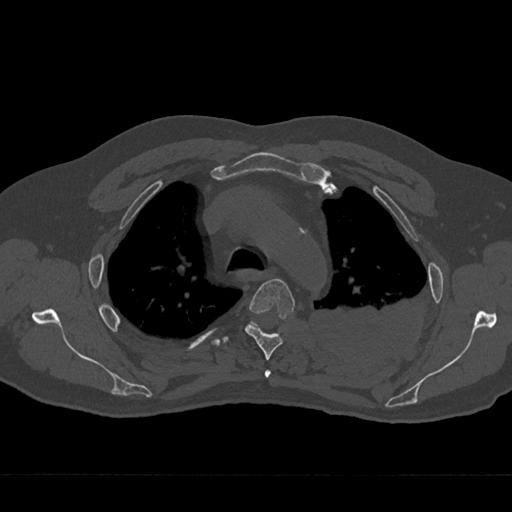
CT including the spine, one axial slice. Slice 517 of 797 in the series (ordered by position). Reconstruction kernel Br40s/3. Bone window (W 1800 / L 400 HU). 512 × 512 image matrix, field of view 377 × 377 mm. Patient: male, 75 years. From the clinical record (not read from this slice): primary cancer: renal.
Structures marked on this image (semi-automatically segmented with operator editing):
- T3 vertebra: bounding box (x1, y1, x2, y2) in pixels: (264, 370, 271, 378)
- T4 vertebra: (224, 278, 295, 360)
- T5 vertebra: (224, 322, 259, 343)